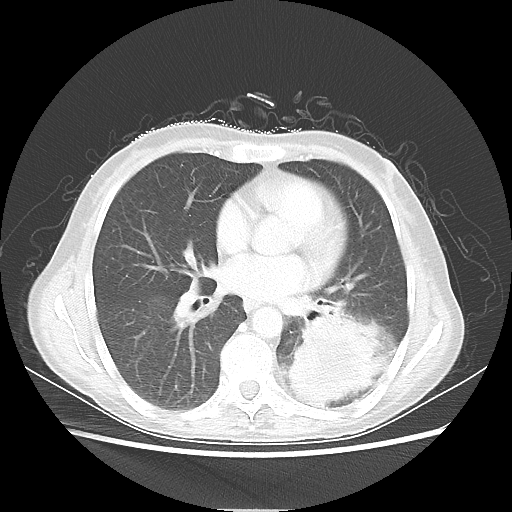
Chest CT, one axial slice; position 27 of 56 along the scan axis; reconstruction kernel LUNG; 80 kVp; lung window (W 1500 / L -600 HU); 5 mm slice thickness; 512 × 512 image matrix. Female patient, age 53 years. From the clinical record (not read from this slice): clinical TNM (as recorded): T3 N0 M0.
Annotated regions visible in this slice (rectangle marked by the reading radiologist):
- lung tumour (recorded histology: adenocarcinoma): bounding box [x1, y1, x2, y2] px = [290, 319, 383, 404]